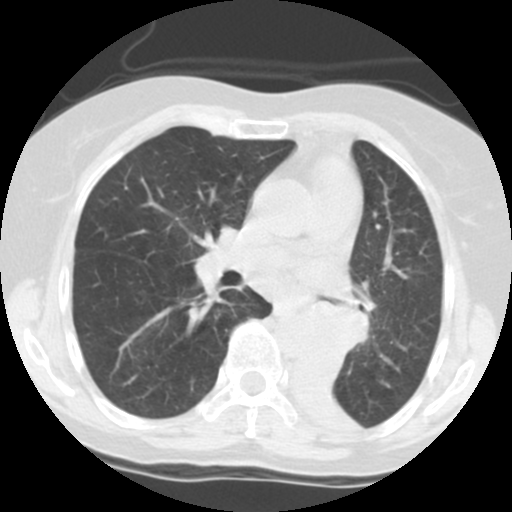
Low-dose screening chest CT, one axial slice. Slice 69 of 113 in the series (ordered by position). Reconstruction kernel STANDARD. 140 kVp. Lung window (W 1500 / L -600 HU). 2.5 mm slice thickness. 512 × 512 image matrix, field of view 280 × 280 mm.
Annotated regions visible in this slice (manually delineated by an expert):
- lesion 1 (tumor, left main bronchus): bounding box <301,299,368,361> (left, top, right, bottom; pixels)